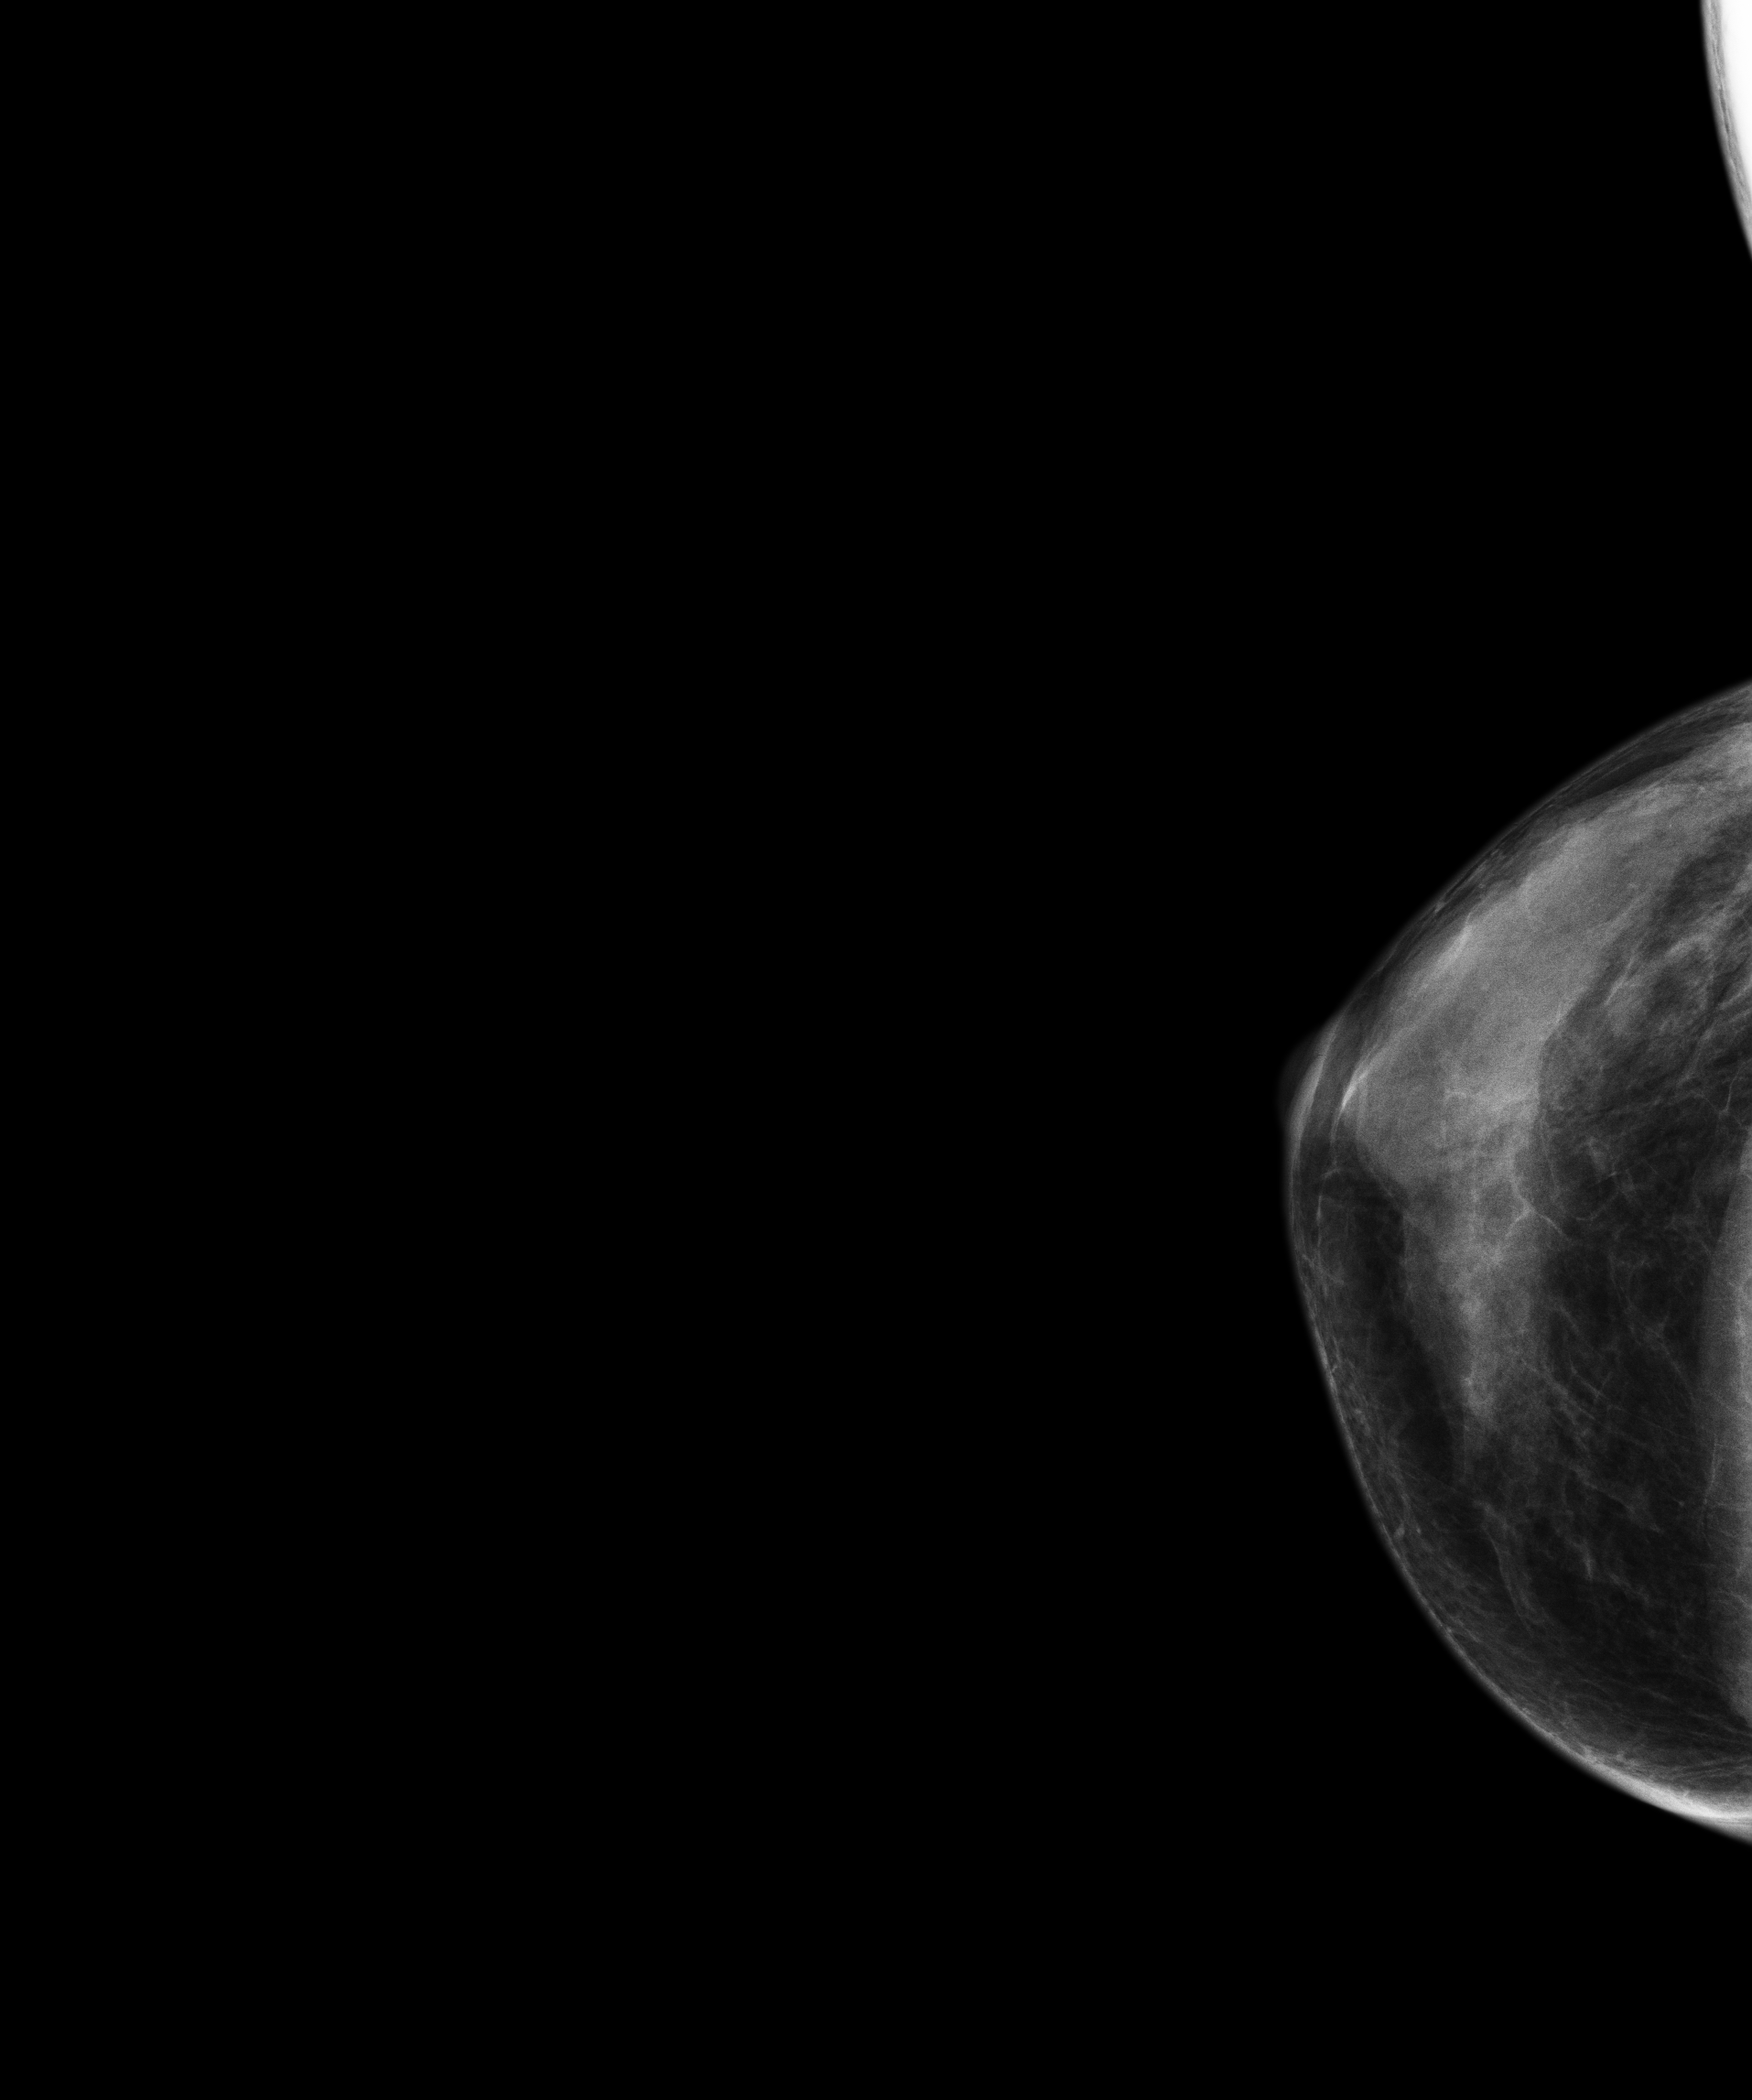
Screening examination; system: Senographe Essential ADS_56.21.3. Patient: female, 56 years.
Image type: full-field digital mammogram. Breast: right. Projection: craniocaudal (CC) view.